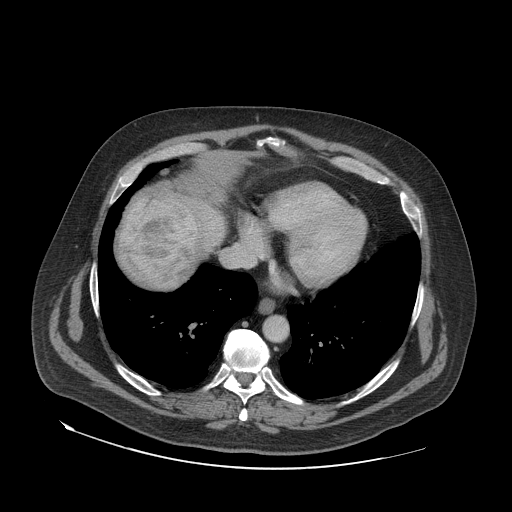
Contrast-enhanced abdominal CT (liver protocol), one axial slice. Position 70 of 79 along the scan axis. Reconstruction kernel STANDARD. Soft-tissue window (W 400 / L 40 HU). 2.5 mm slice thickness. 512 × 512 image matrix. Case-level facts recorded for this patient, not image findings: diagnosis: hepatocellular carcinoma (patient treated with transarterial chemoembolisation; whether this scan precedes or follows treatment is not stated here); TNM stage (as recorded): Stage-IVA; Child-Pugh class: A; tumour differentiation: well differentiated; tumour nodularity: multinodular.
Annotated regions visible in this slice (semi-automatic segmentation, software-assisted and operator-edited):
- liver parenchyma outside the tumour (the mass and vessels are separate outlines, so this box may not span the whole liver): bounding box (x1, y1, x2, y2) in pixels: (120, 194, 226, 290)
- mass: (121, 193, 199, 284)